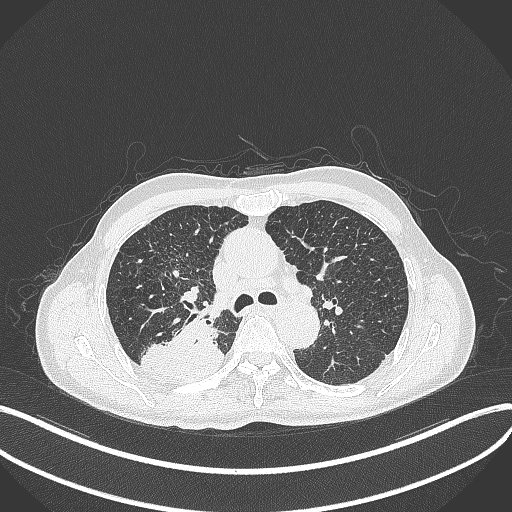
Chest CT, one axial slice; slice 302 of 428 in the series (ordered by position); reconstruction kernel B70f; 120 kVp; lung window (W 1500 / L -600 HU); 1 mm slice thickness; 512 × 512 image matrix, field of view 400 × 400 mm. Male patient, age 79 years. Case-level facts recorded for this patient, not image findings: clinical TNM (as recorded): T3 N0 M0.
Annotated regions visible in this slice (bounding box drawn by a radiologist):
- lung tumour (recorded histology: adenocarcinoma): bounding box (x1, y1, x2, y2) in pixels: (141, 319, 225, 383)